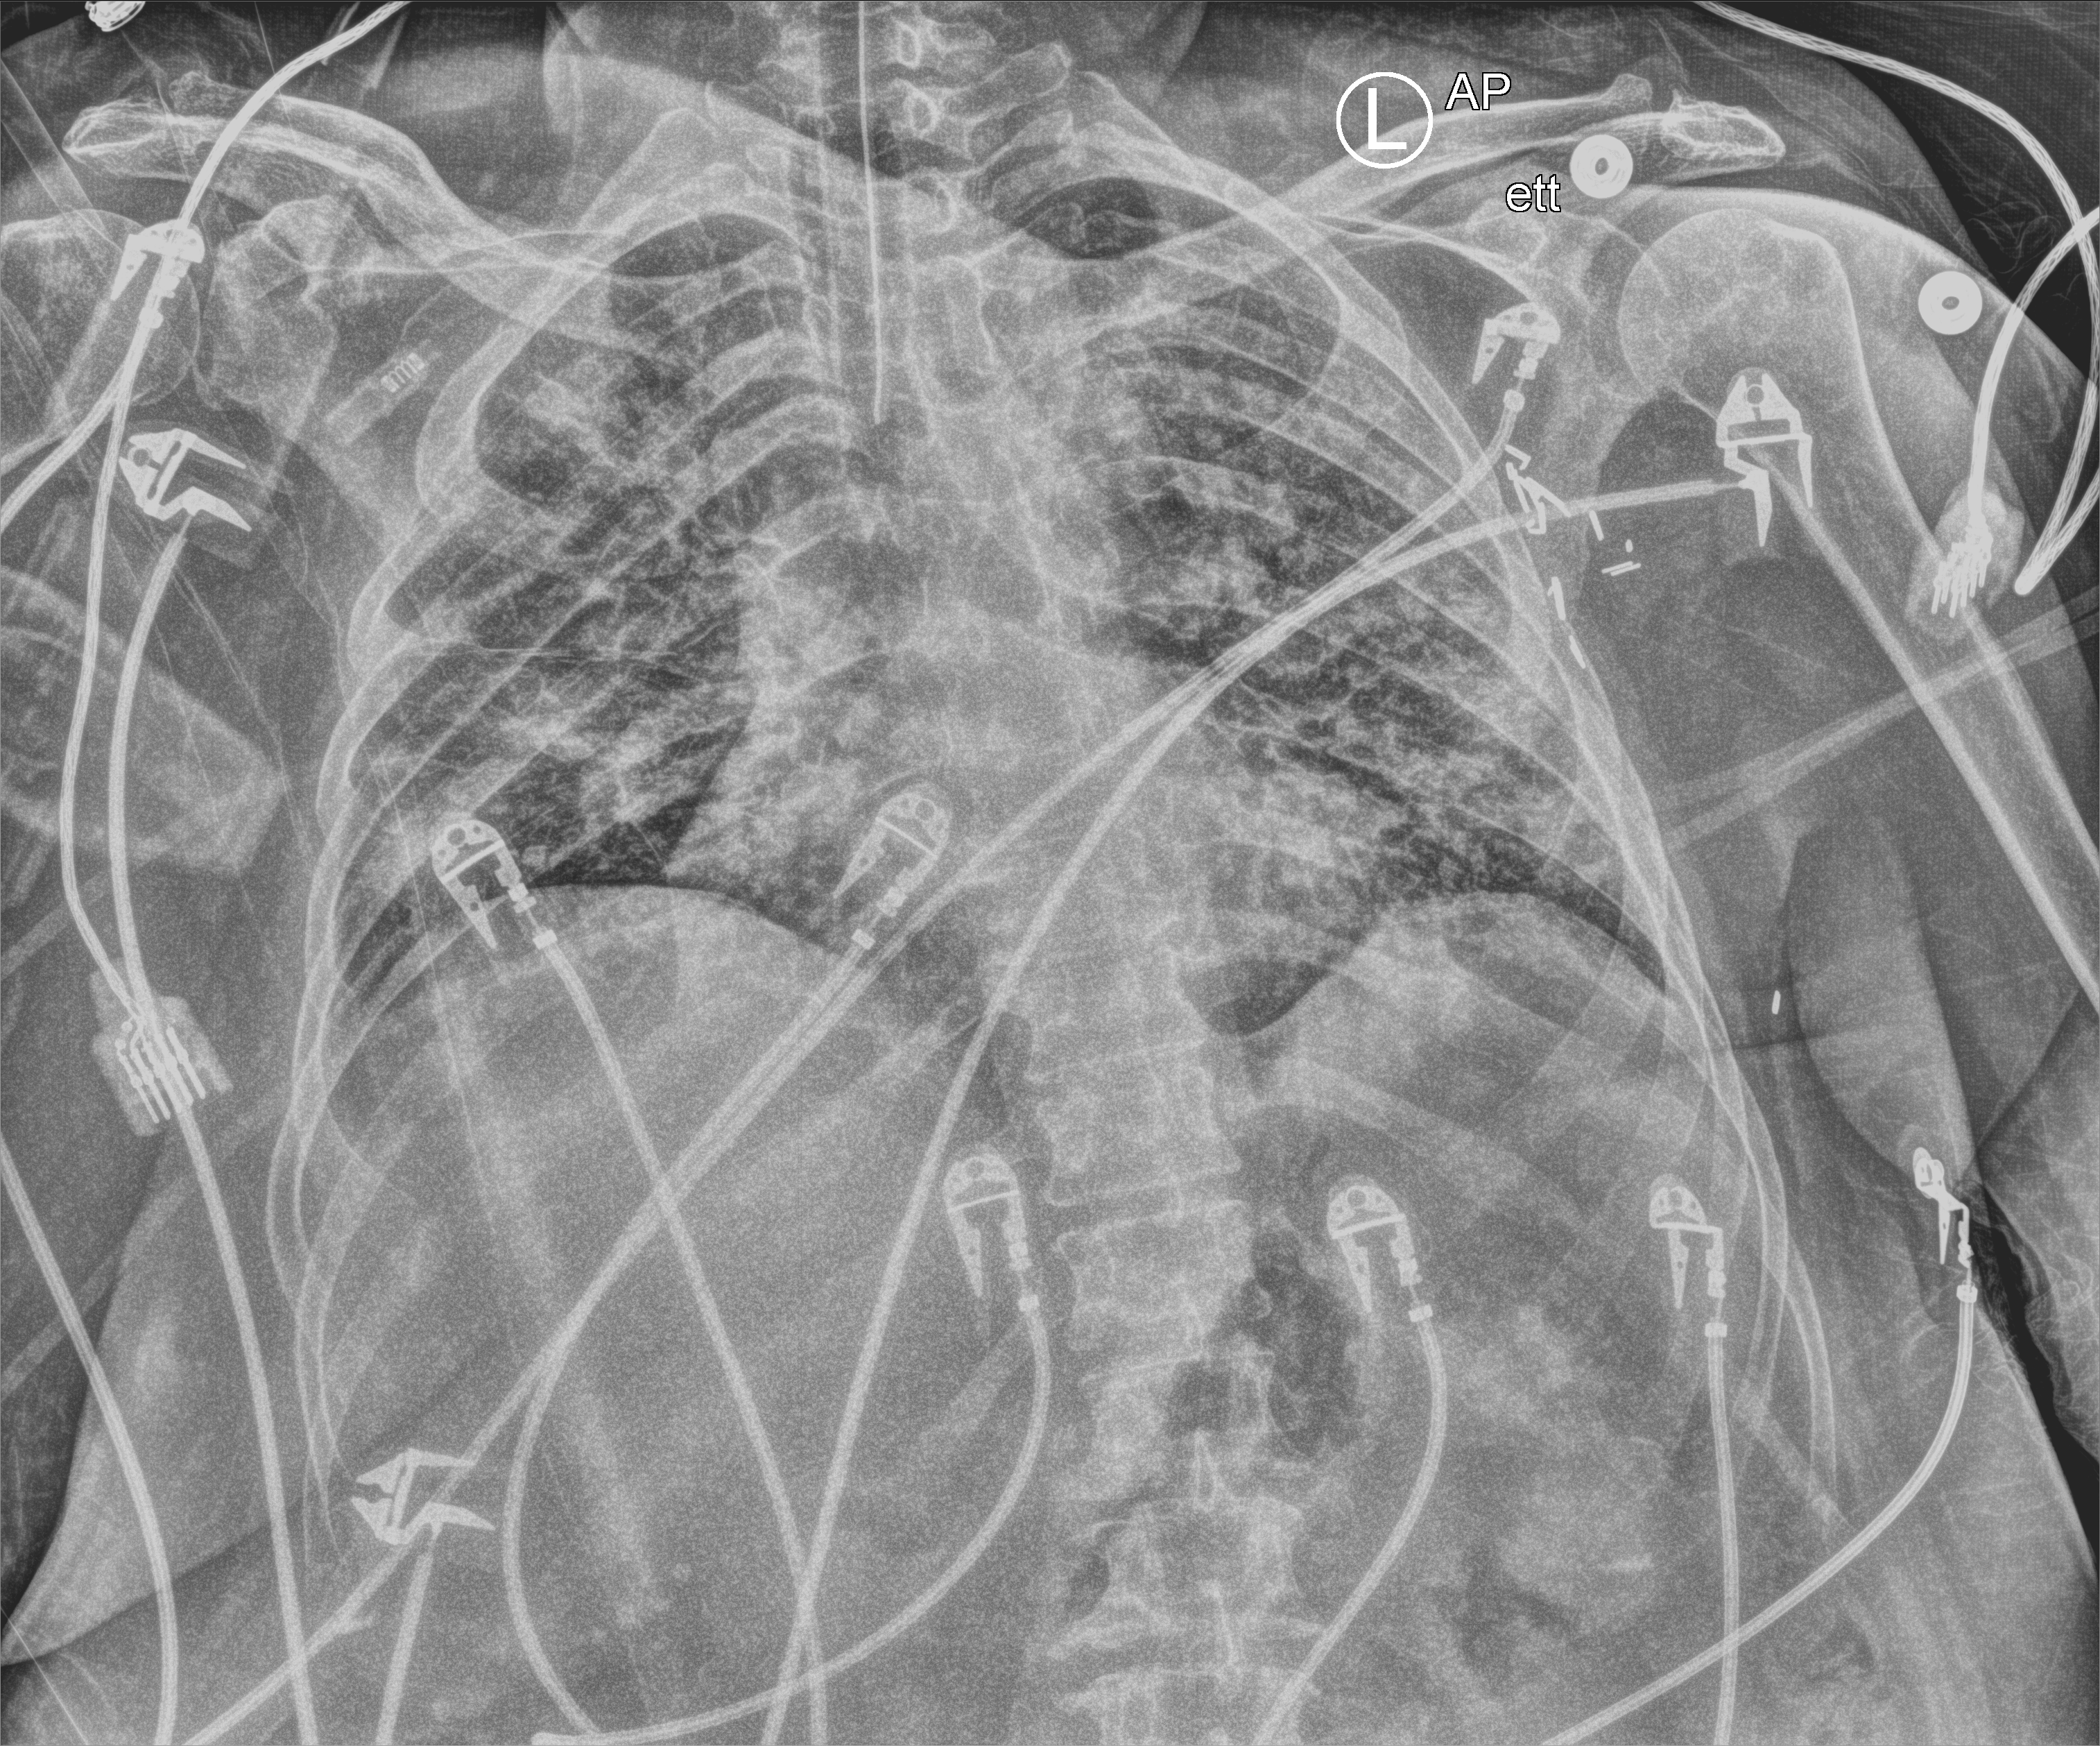
Portable chest radiograph; anteroposterior (AP) projection. Patient hospitalised with COVID-19; female, aged 60–74 years.
Admission-level facts for this patient (not findings on this image; timing relative to this image not recorded):
- COPD (admission record): no